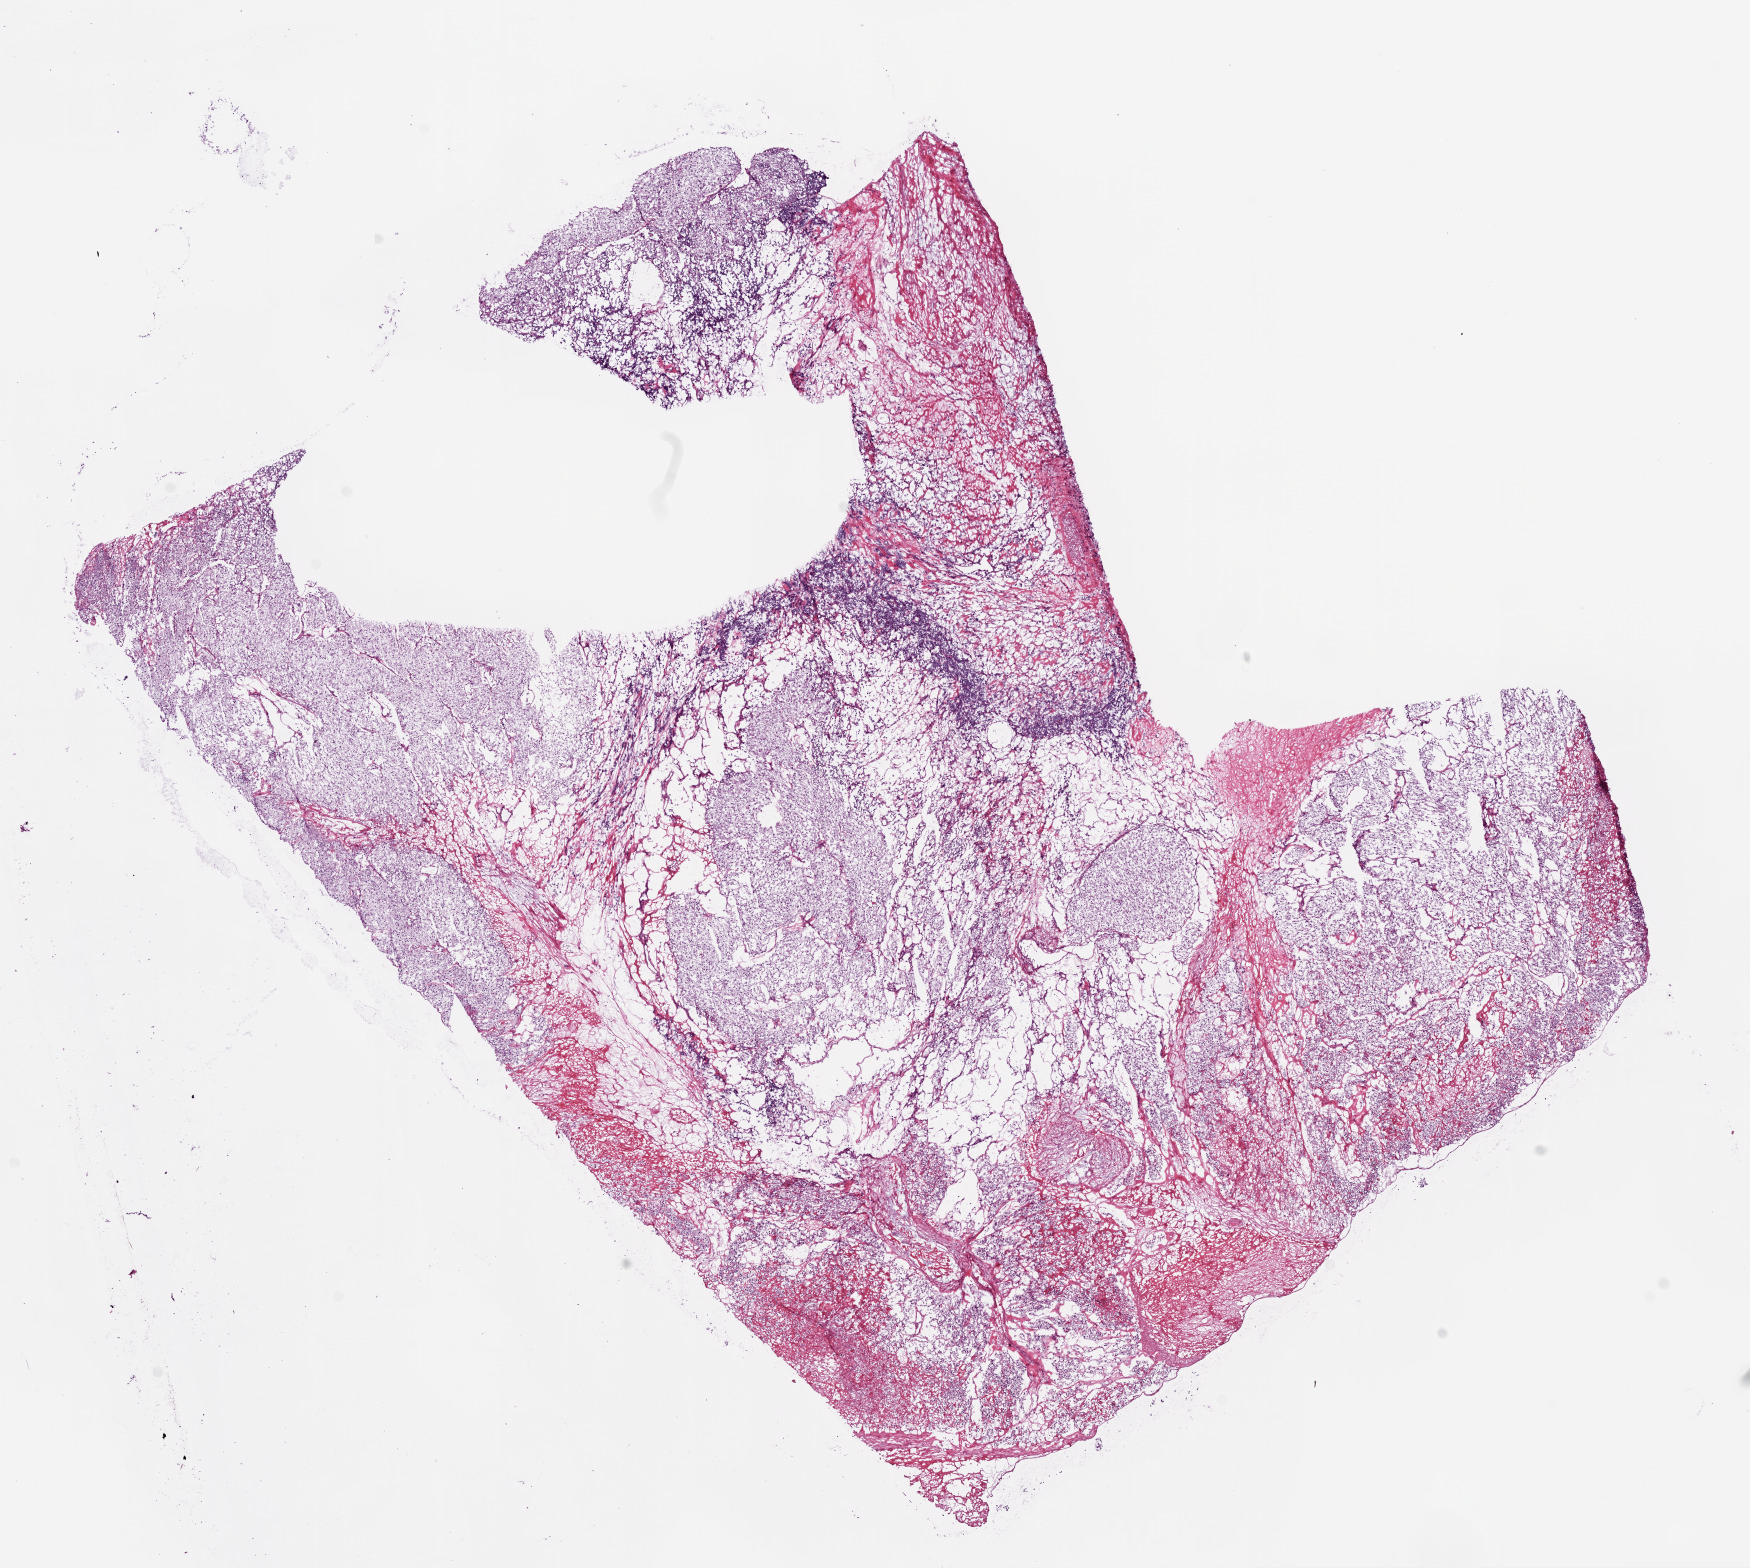
Whole-slide histology image, H&E-stained — whole scanned area (about 14.0 x 12.6 mm, acquisition: 20x scan) shown as a low-resolution overview, frozen section, sample: primary tumour, kidney. Male, age 45 years at initial diagnosis. Histologic grade: G2 (moderately differentiated). Slide review estimates, as recorded: tumour cells 90%, tumour nuclei 75%, normal cells 0%, stromal cells 10%, necrosis 0%. Infiltration values recorded for this section: lymphocyte infiltration 15%, monocyte infiltration 0%, neutrophil infiltration 0%.
AJCC pathologic stage: II (6th edition). Histologic diagnosis: Clear cell adenocarcinoma, NOS. Laterality: left. TNM: T2 N0 M0.